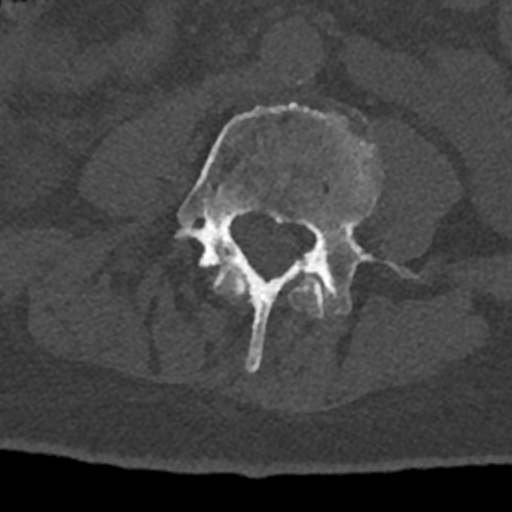
CT including the spine, one axial slice; position 268 of 797 along the scan axis; reconstruction kernel Br40s/3; 120 kVp; bone window (W 1800 / L 400 HU); 0.5 mm slice thickness; 512 × 512 image matrix. Patient: male, 74 years. From the clinical record (not read from this slice): primary cancer: renal; vertebrae with lytic lesions (as recorded): T10, L1, L2, L3, L4, L5.
Annotated regions visible in this slice (semi-automatically segmented with operator editing):
- L3 vertebra: bounding box (x1, y1, x2, y2) in pixels: (213, 265, 331, 318)
- L4 vertebra: (175, 102, 419, 373)